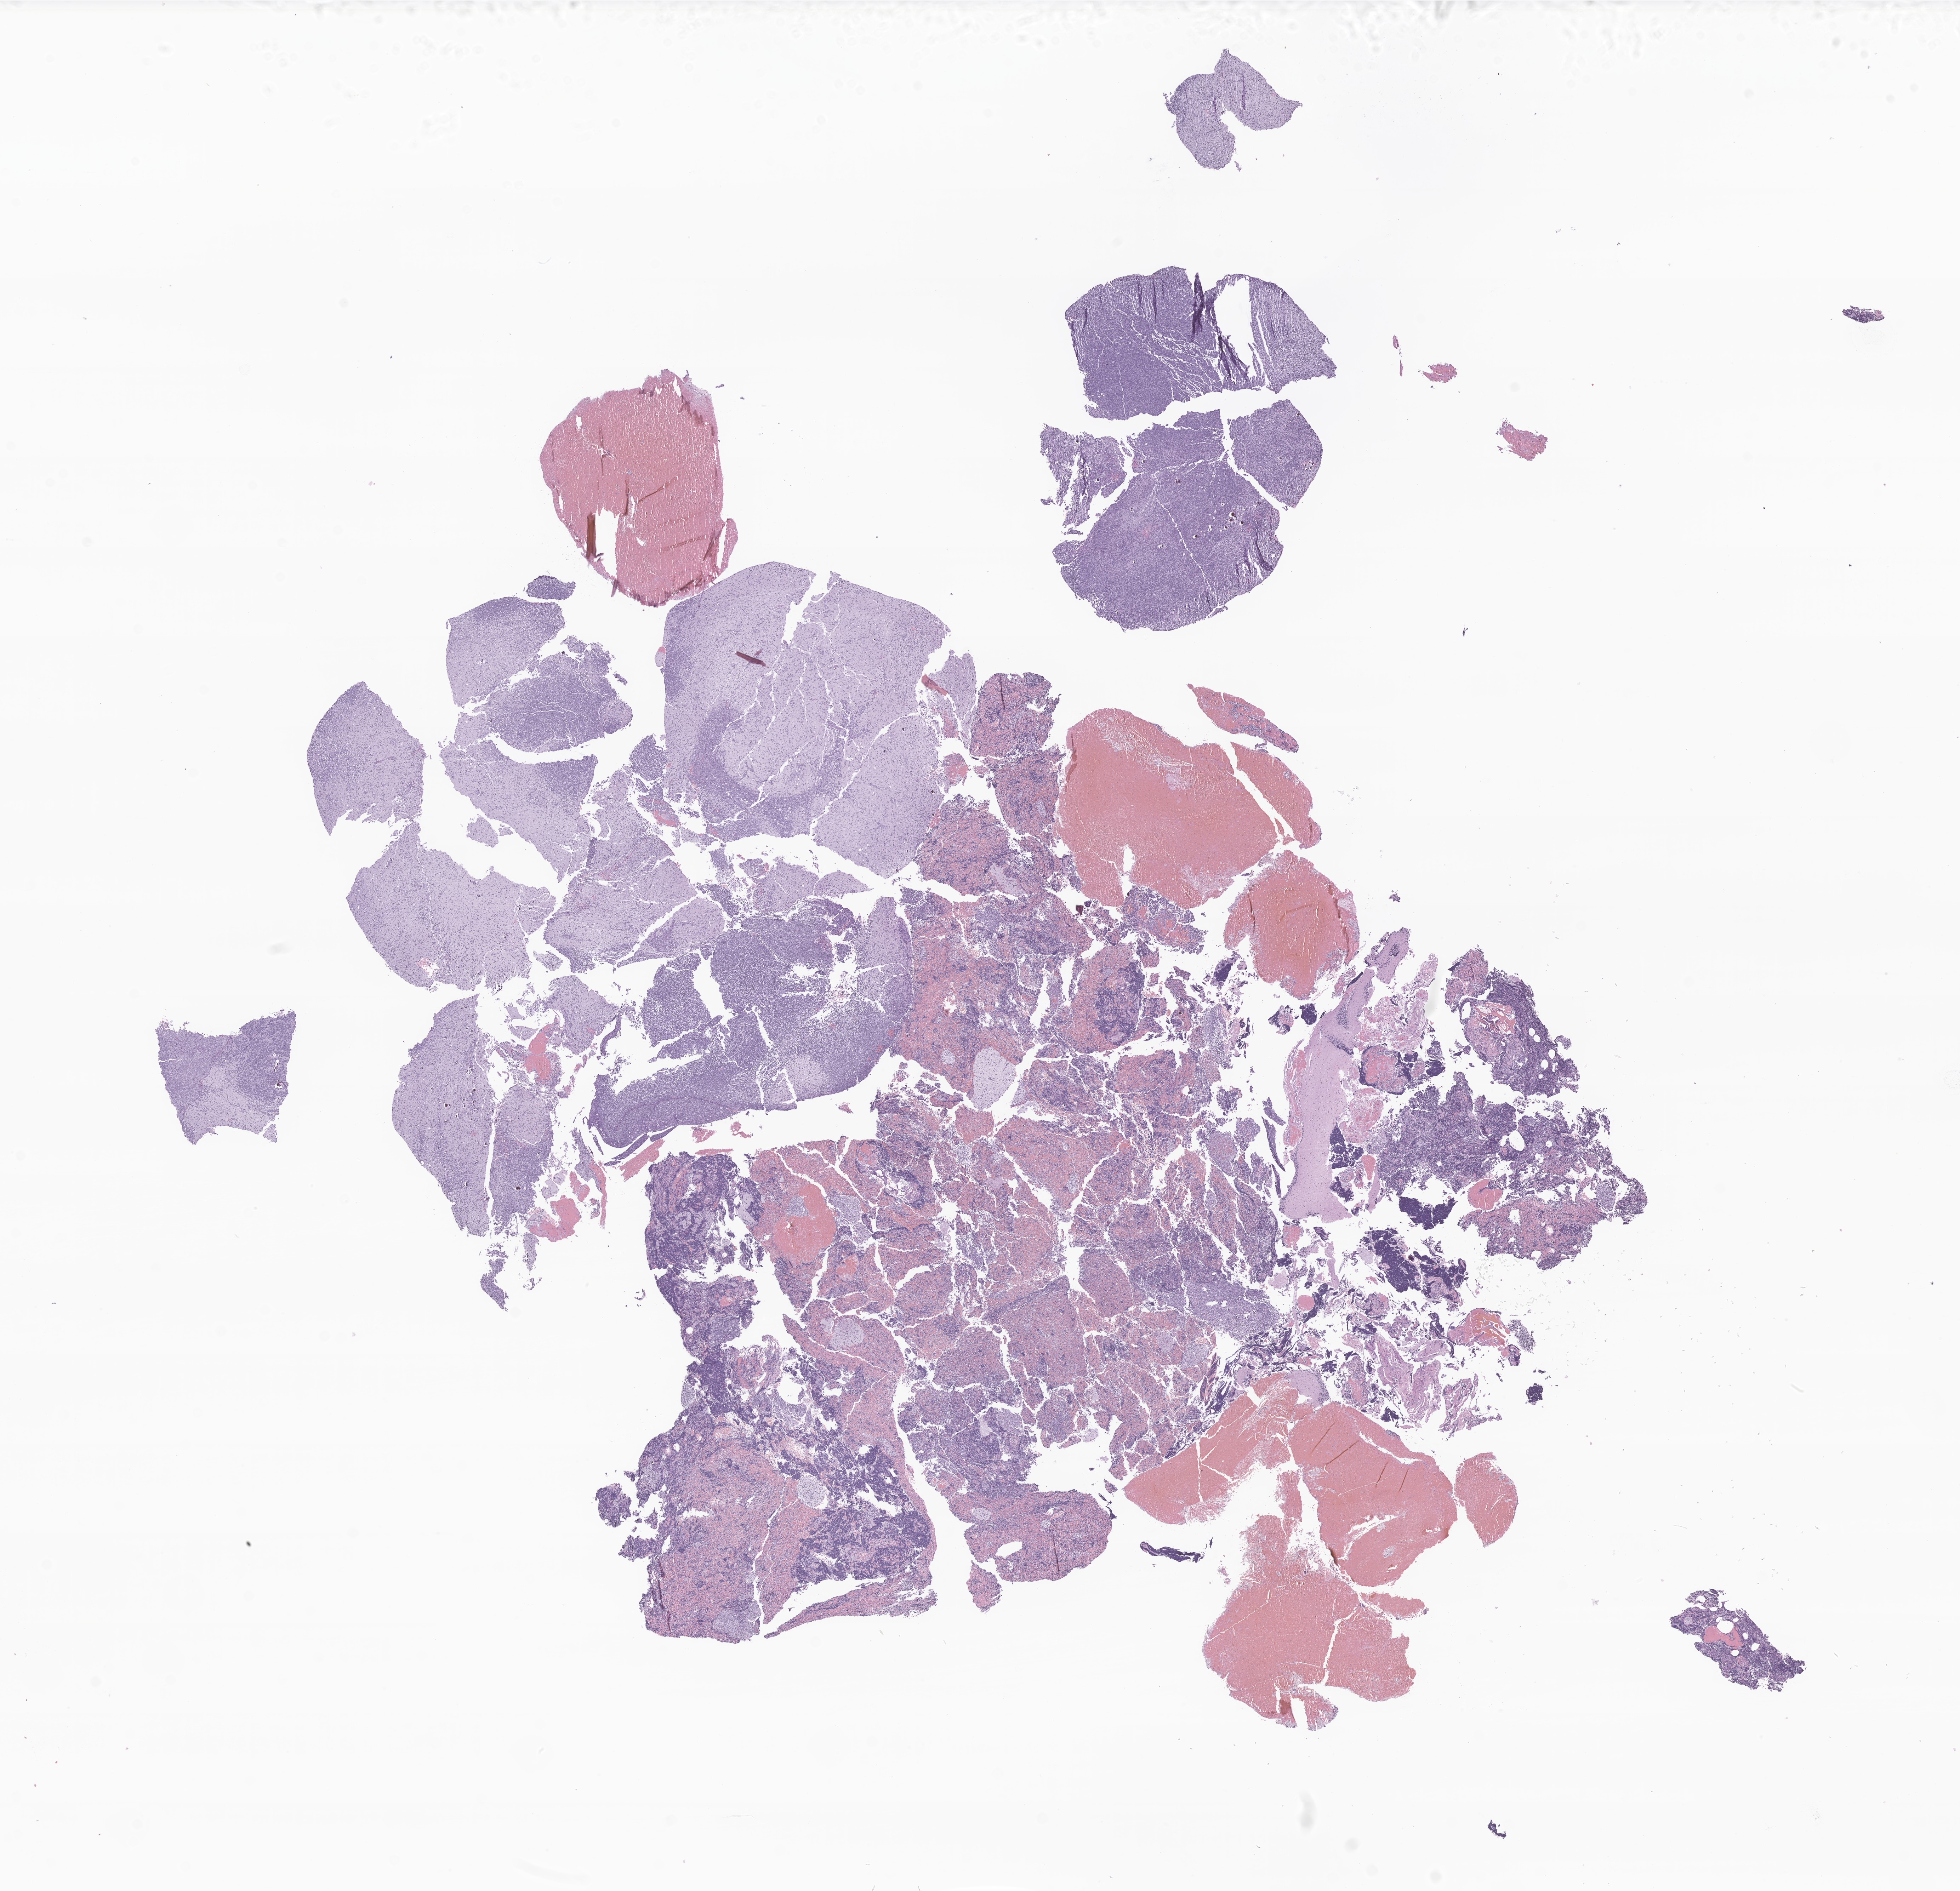
H&E whole-slide image of tumor tissue from the brain — shown as a low-resolution overview of the whole scanned area (about 23.3 x 22.5 mm), formalin-fixed, paraffin-embedded (FFPE) tissue. Male patient, age 496 days (about 1.4 years).
Diagnosis: Medulloblastoma, NOS.